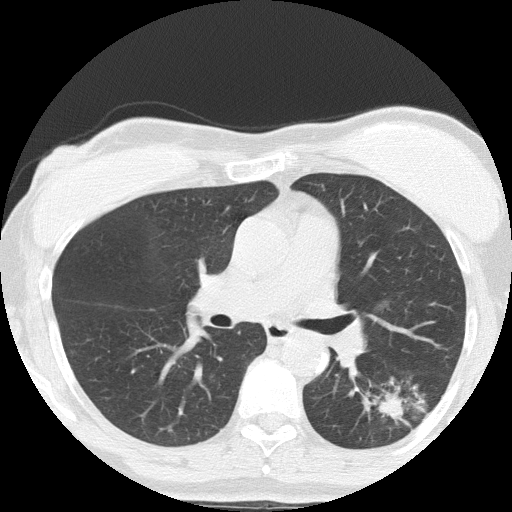
Low-dose screening chest CT, axial slice. Third screening round (two years after baseline). Lung window (W 1500 / L -600 HU). Lung (sharp) reconstruction kernel (FC51). 120 kVp. Slice 66 of 152 in the series. 512 × 512 image matrix. Female, age 64 years at enrolment. Former smoker at enrolment.
- Expert-annotated lung lesion, bounding box (x1, y1, x2, y2) in pixels: (360, 372, 449, 446).
- The screening reader recorded 3 non-calcified nodules or masses ≥4 mm on this exam (right upper lobe, left lower lobe, right middle lobe); which of them this box marks is not recorded.
- Official screen result: positive, other.
- Participant outcome: lung cancer diagnosed 212 days after this screen — adenocarcinoma, NOS, left lower lobe, moderately differentiated (G2), stage IA (AJCC 6th edition), 17 mm at pathology.